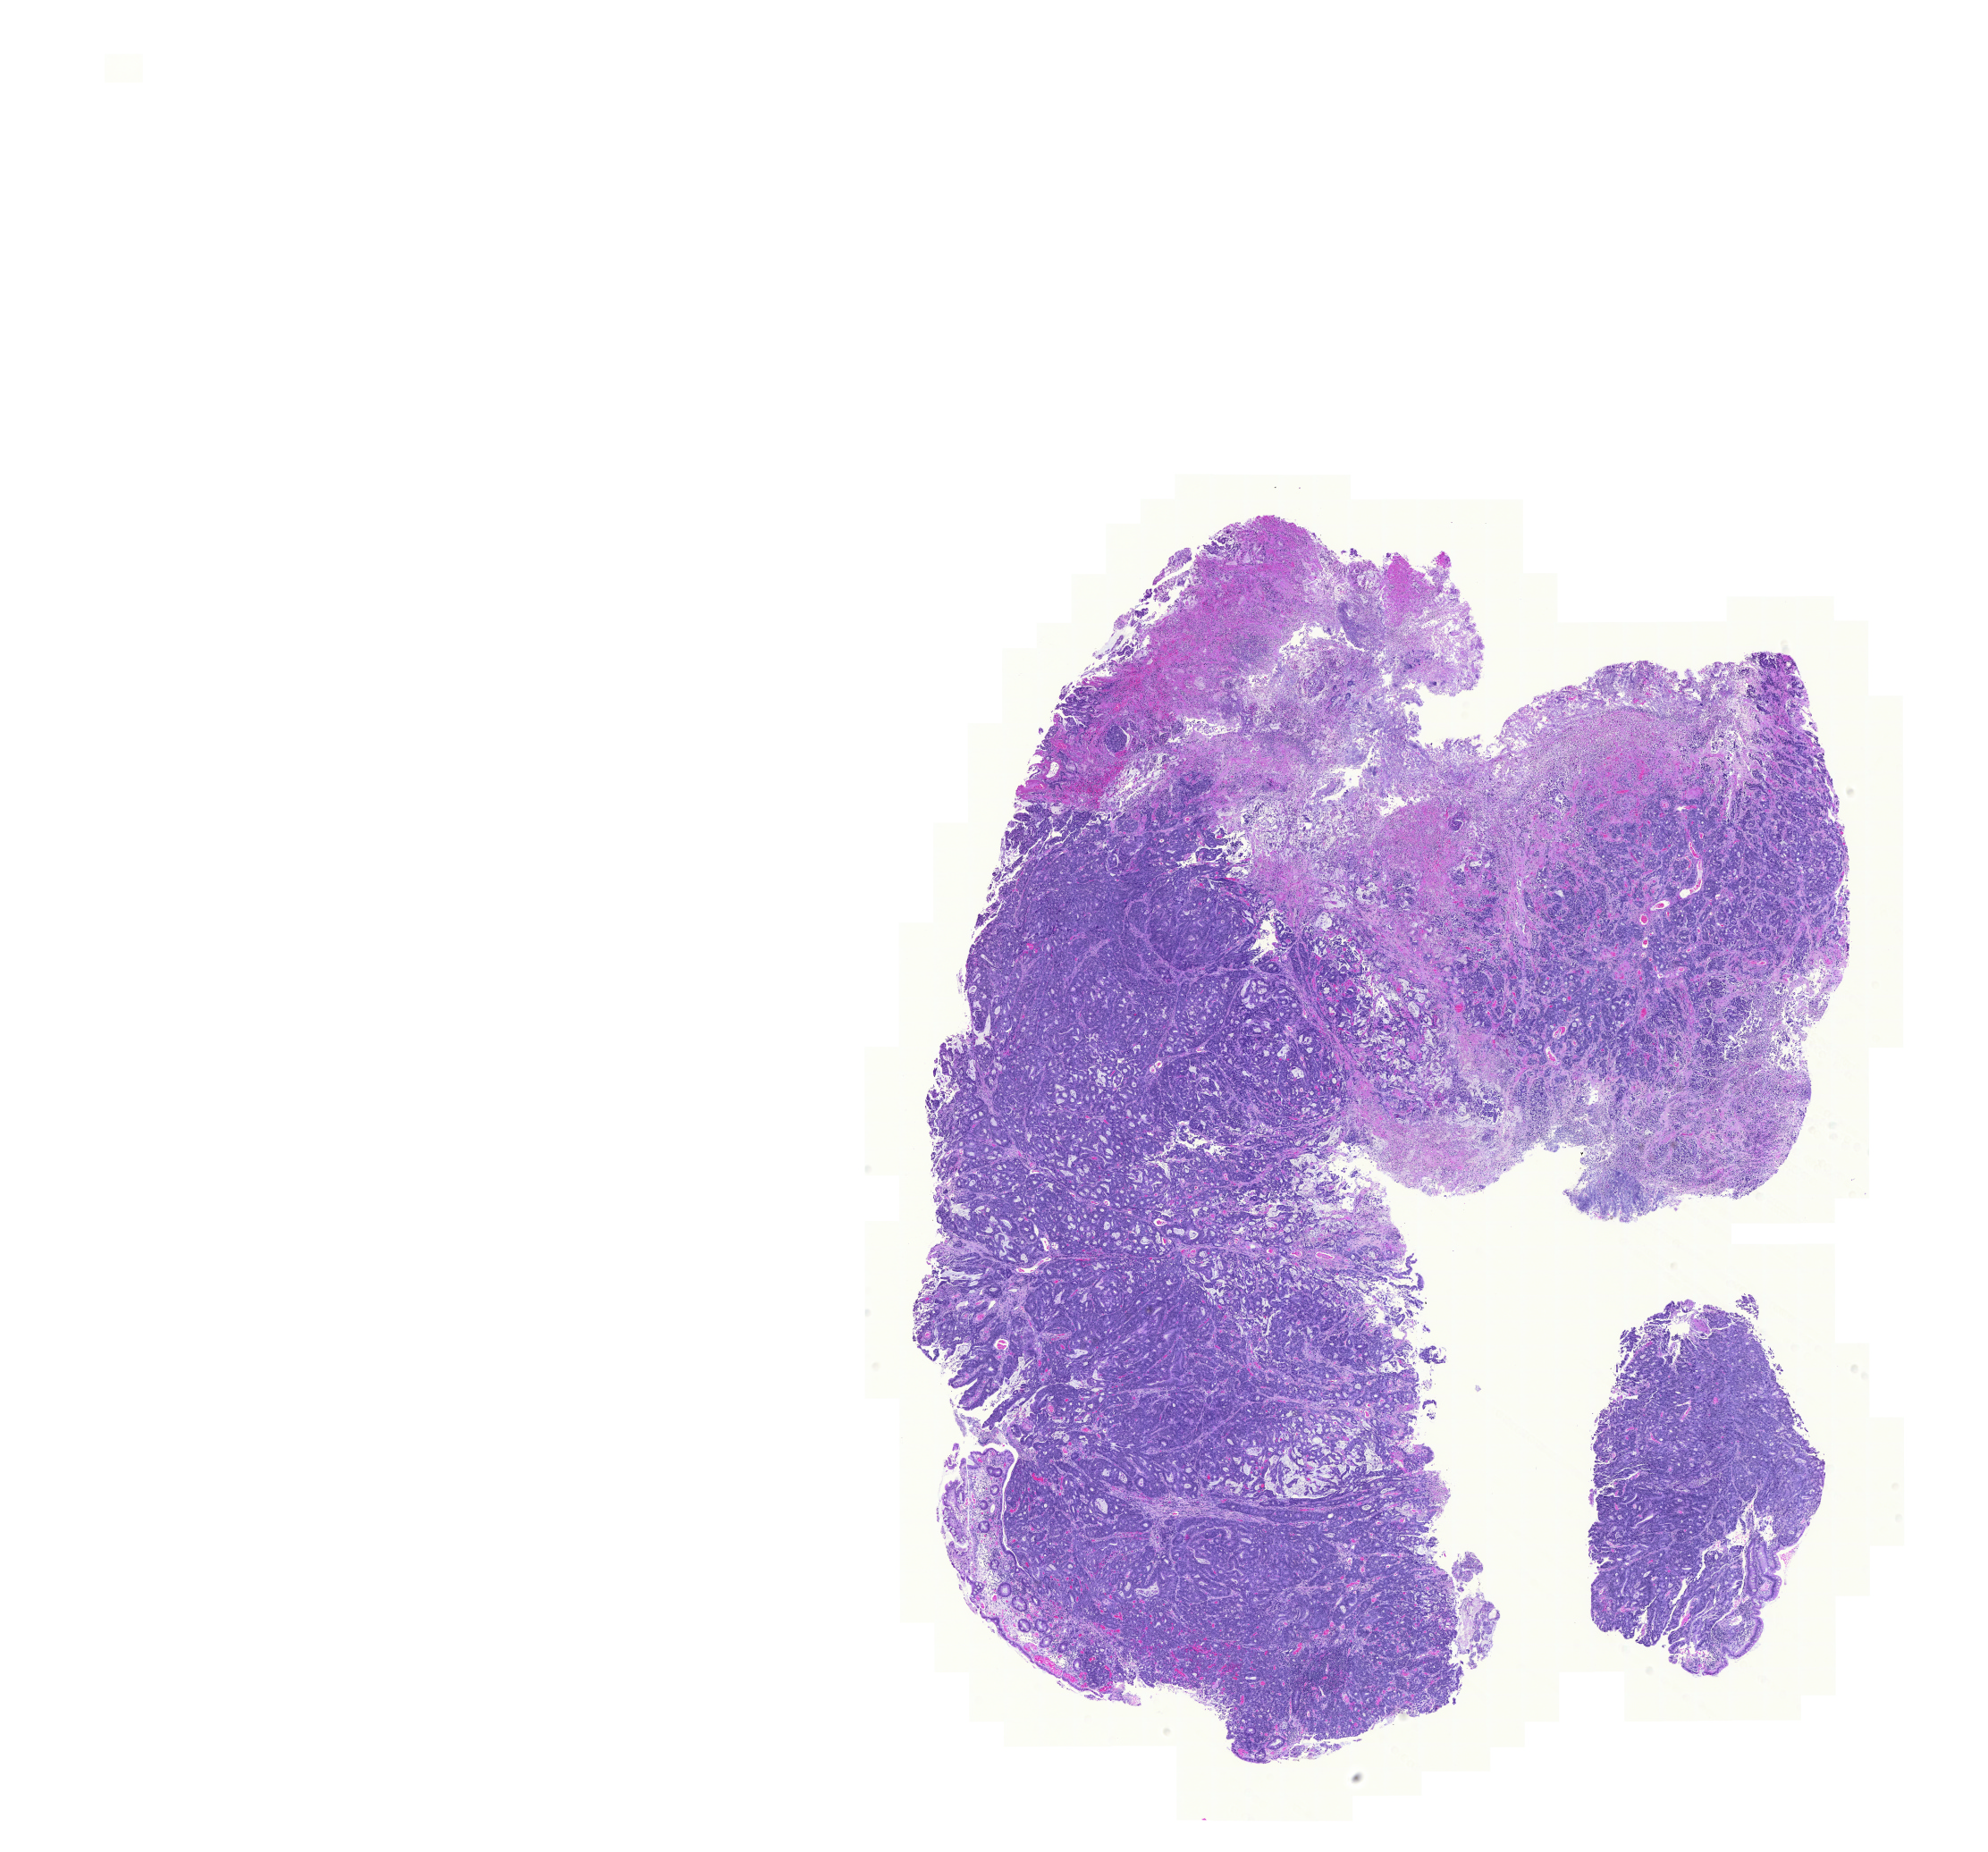
H&E-stained whole-slide image, shown as a low-resolution overview of the whole scanned area (about 16.5 x 15.4 mm); FFPE section; primary tumour sample from the colon. Male patient; age at initial diagnosis 64 years.
- lymph nodes positive (case pathology): 0 of 41 examined
- AJCC pathologic stage: IIA
- pathologic diagnosis: Adenocarcinoma, NOS (ascending colon)
- TNM: T3 N0 M0